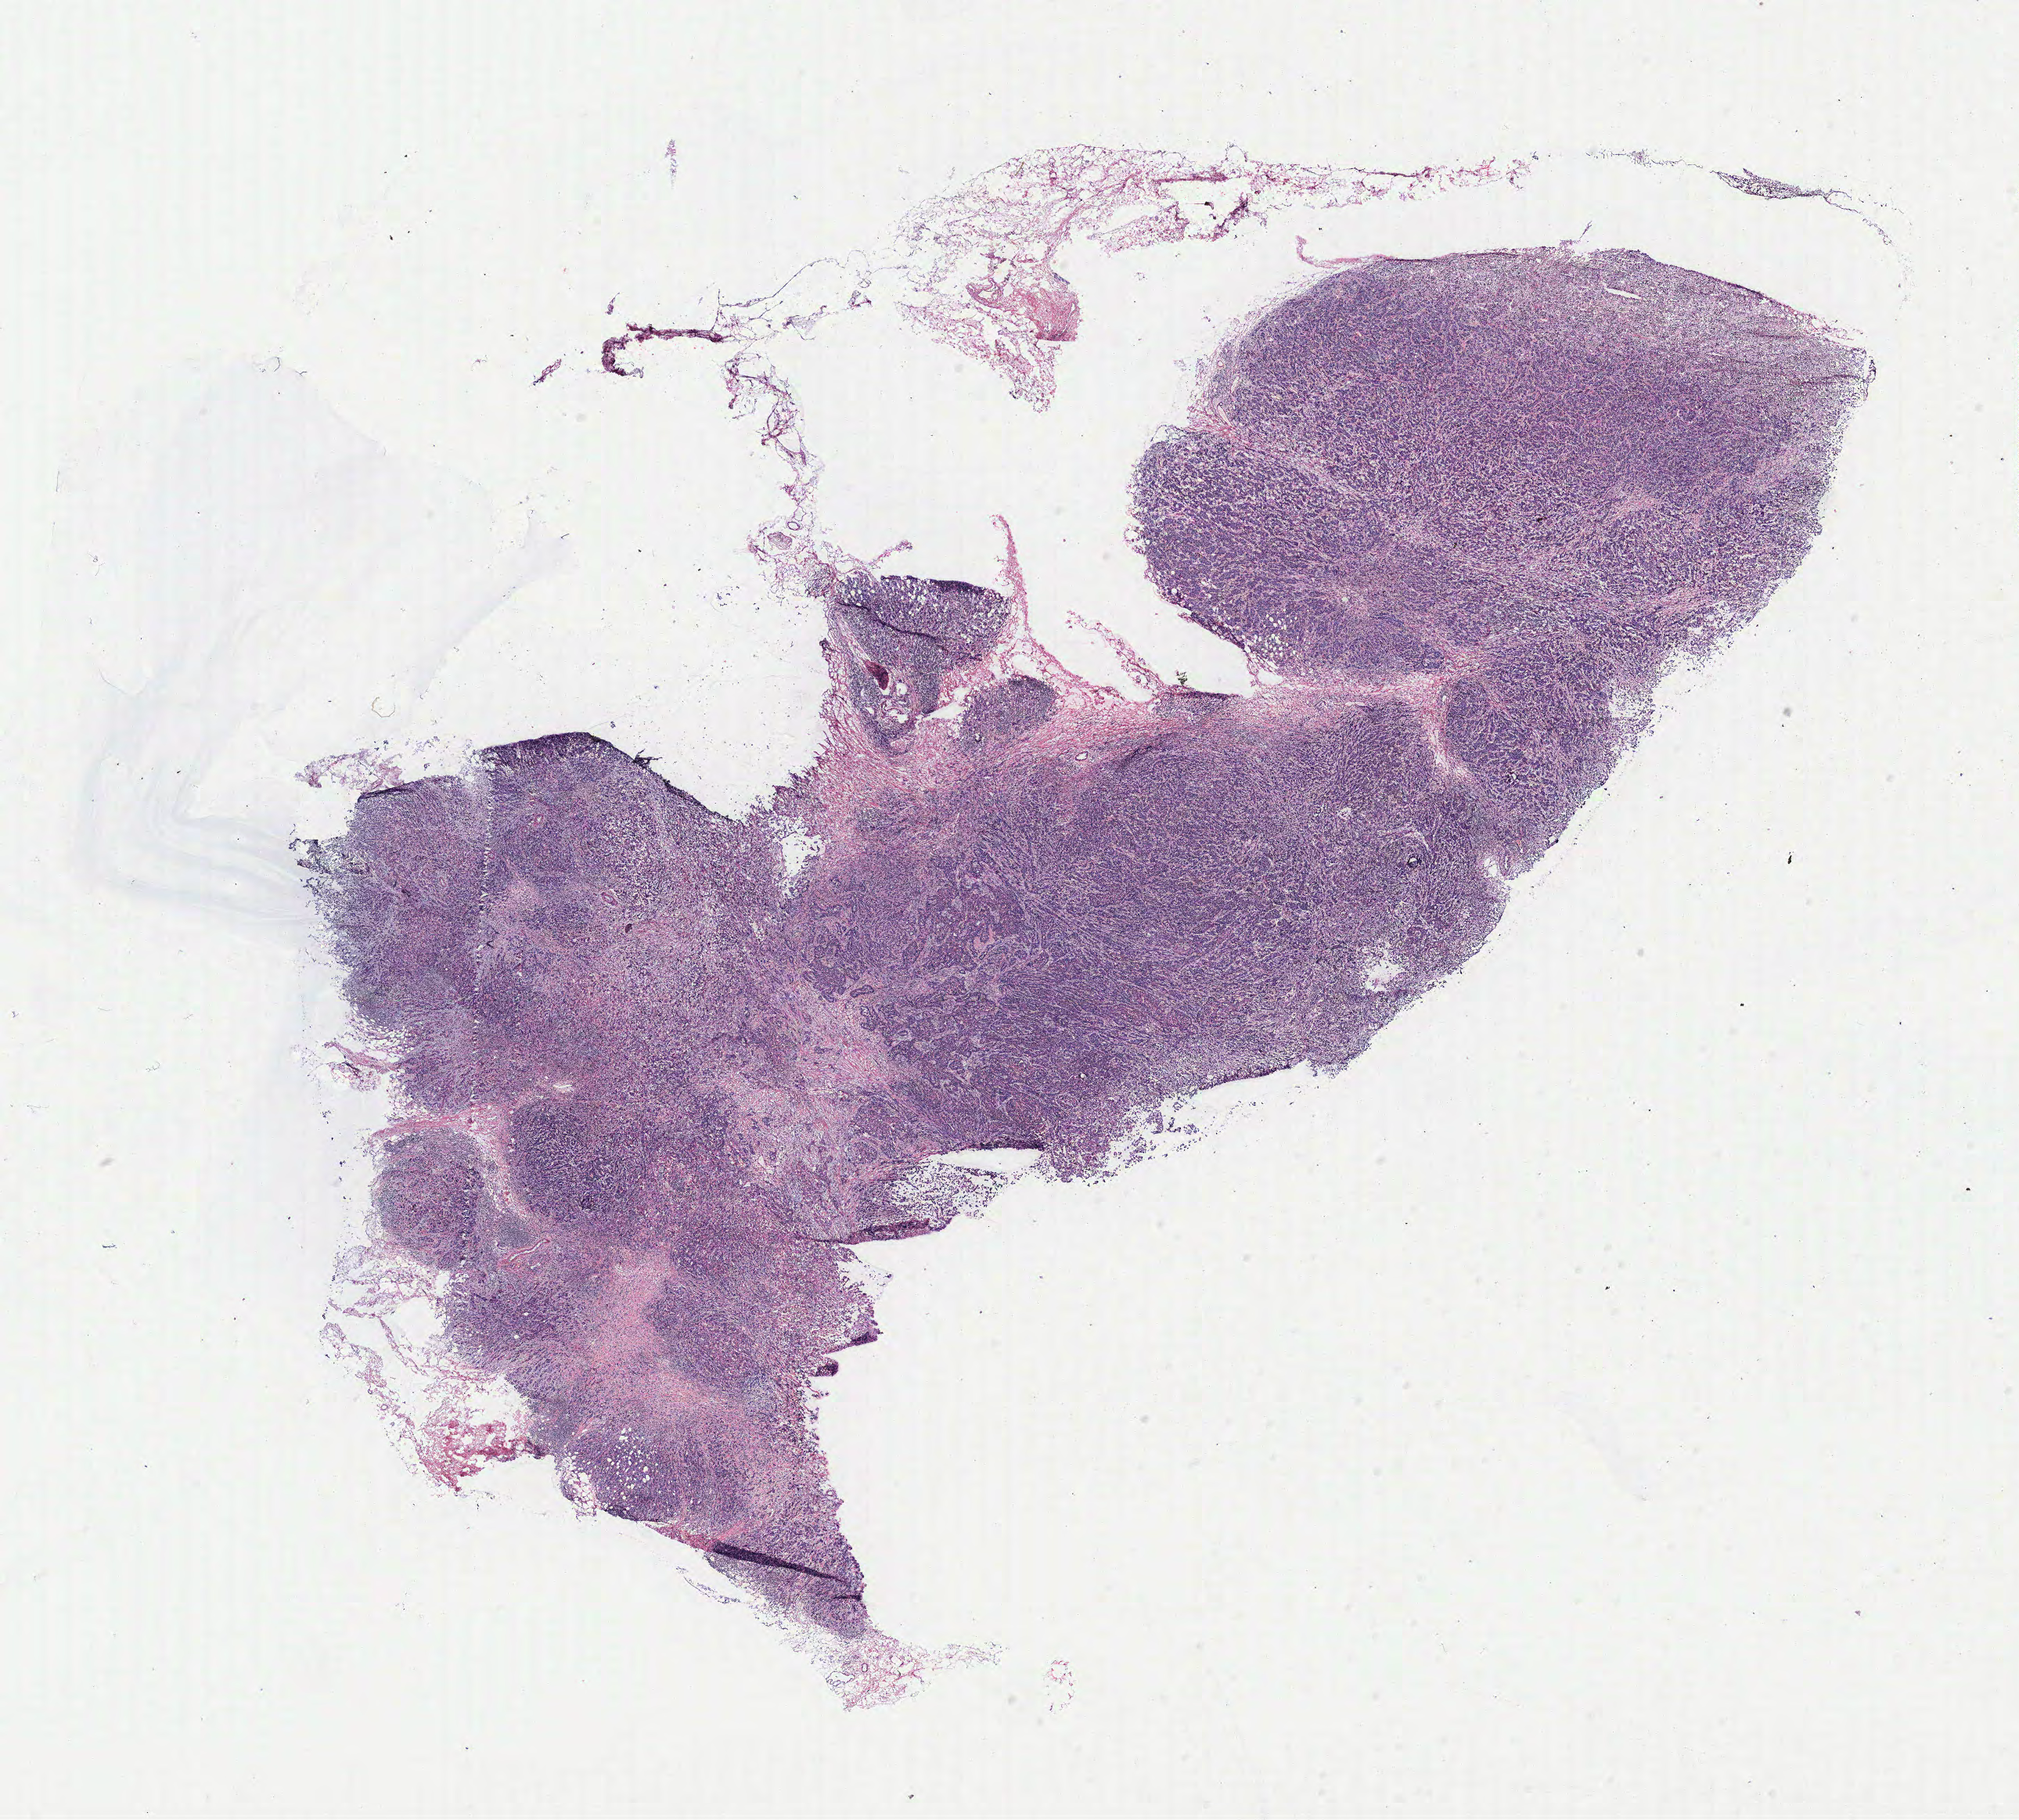
H&E-stained whole-slide image, whole scanned area (about 20.6 x 18.6 mm, slide scanned at 40x) shown as a low-resolution overview. Breast, tissue type not recorded. Female, 47 y/o.
Patient diagnosis: Infiltrating duct carcinoma, NOS.